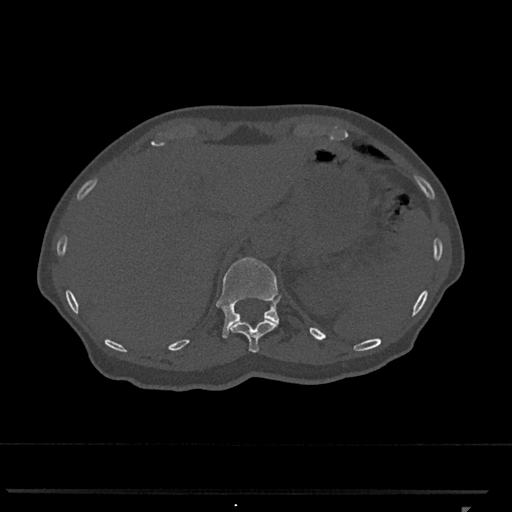
CT including the spine, one axial slice. Position 489 of 793 along the scan axis. Bone window (W 1800 / L 400 HU). 512 × 512 image matrix, field of view 380 × 380 mm. Patient: female, 62 years. Case-level facts recorded for this patient, not image findings: primary cancer: renal.
Outlined on this slice (semi-automatically segmented with operator editing):
- T11 vertebra: bounding box (x1, y1, x2, y2) in pixels: (230, 319, 278, 353)
- T12 vertebra: (216, 257, 281, 338)